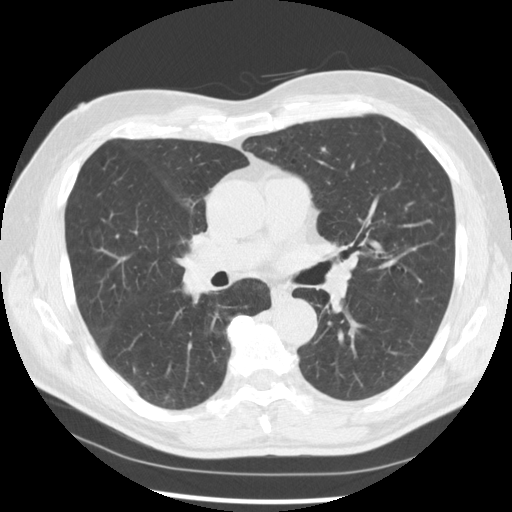
Low-dose screening chest CT, one axial slice; slice 159 of 277 in the series (ordered by position); reconstruction kernel STANDARD; 120 kVp; lung window (W 1500 / L -600 HU); 512 × 512 image matrix, field of view 365 × 365 mm.
Outlined on this slice (expert manual segmentation):
- lesion 1 (tumor, middle lobe of right lung): bounding box <183,266,214,300> (left, top, right, bottom; pixels)